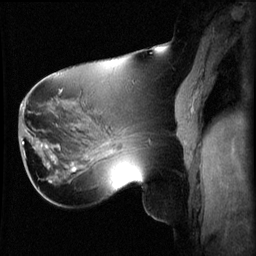
Breast MRI (dynamic contrast-enhanced), one sagittal slice; slice 27 of 60 in the series (ordered by position); 3 images stored at this slice position (order not interpretable as contrast timing); 1.5 T; TE 4.2 ms, TR 8.2 ms; 2.2 mm slice thickness; 256 × 256 image matrix, field of view 220 × 220 mm. Female patient, age 62 years.
Outlined on this slice (semi-automatic segmentation, software-assisted and operator-edited):
- analysis volume of interest (the breast-tissue region the enhancement analysis was run in; not a lesion): bounding box (x1, y1, x2, y2) in pixels: (26, 126, 59, 165)
- tumour enhancement mask (voxels above the 70 % enhancement threshold inside the analysis volume of interest): (32, 138, 49, 149)